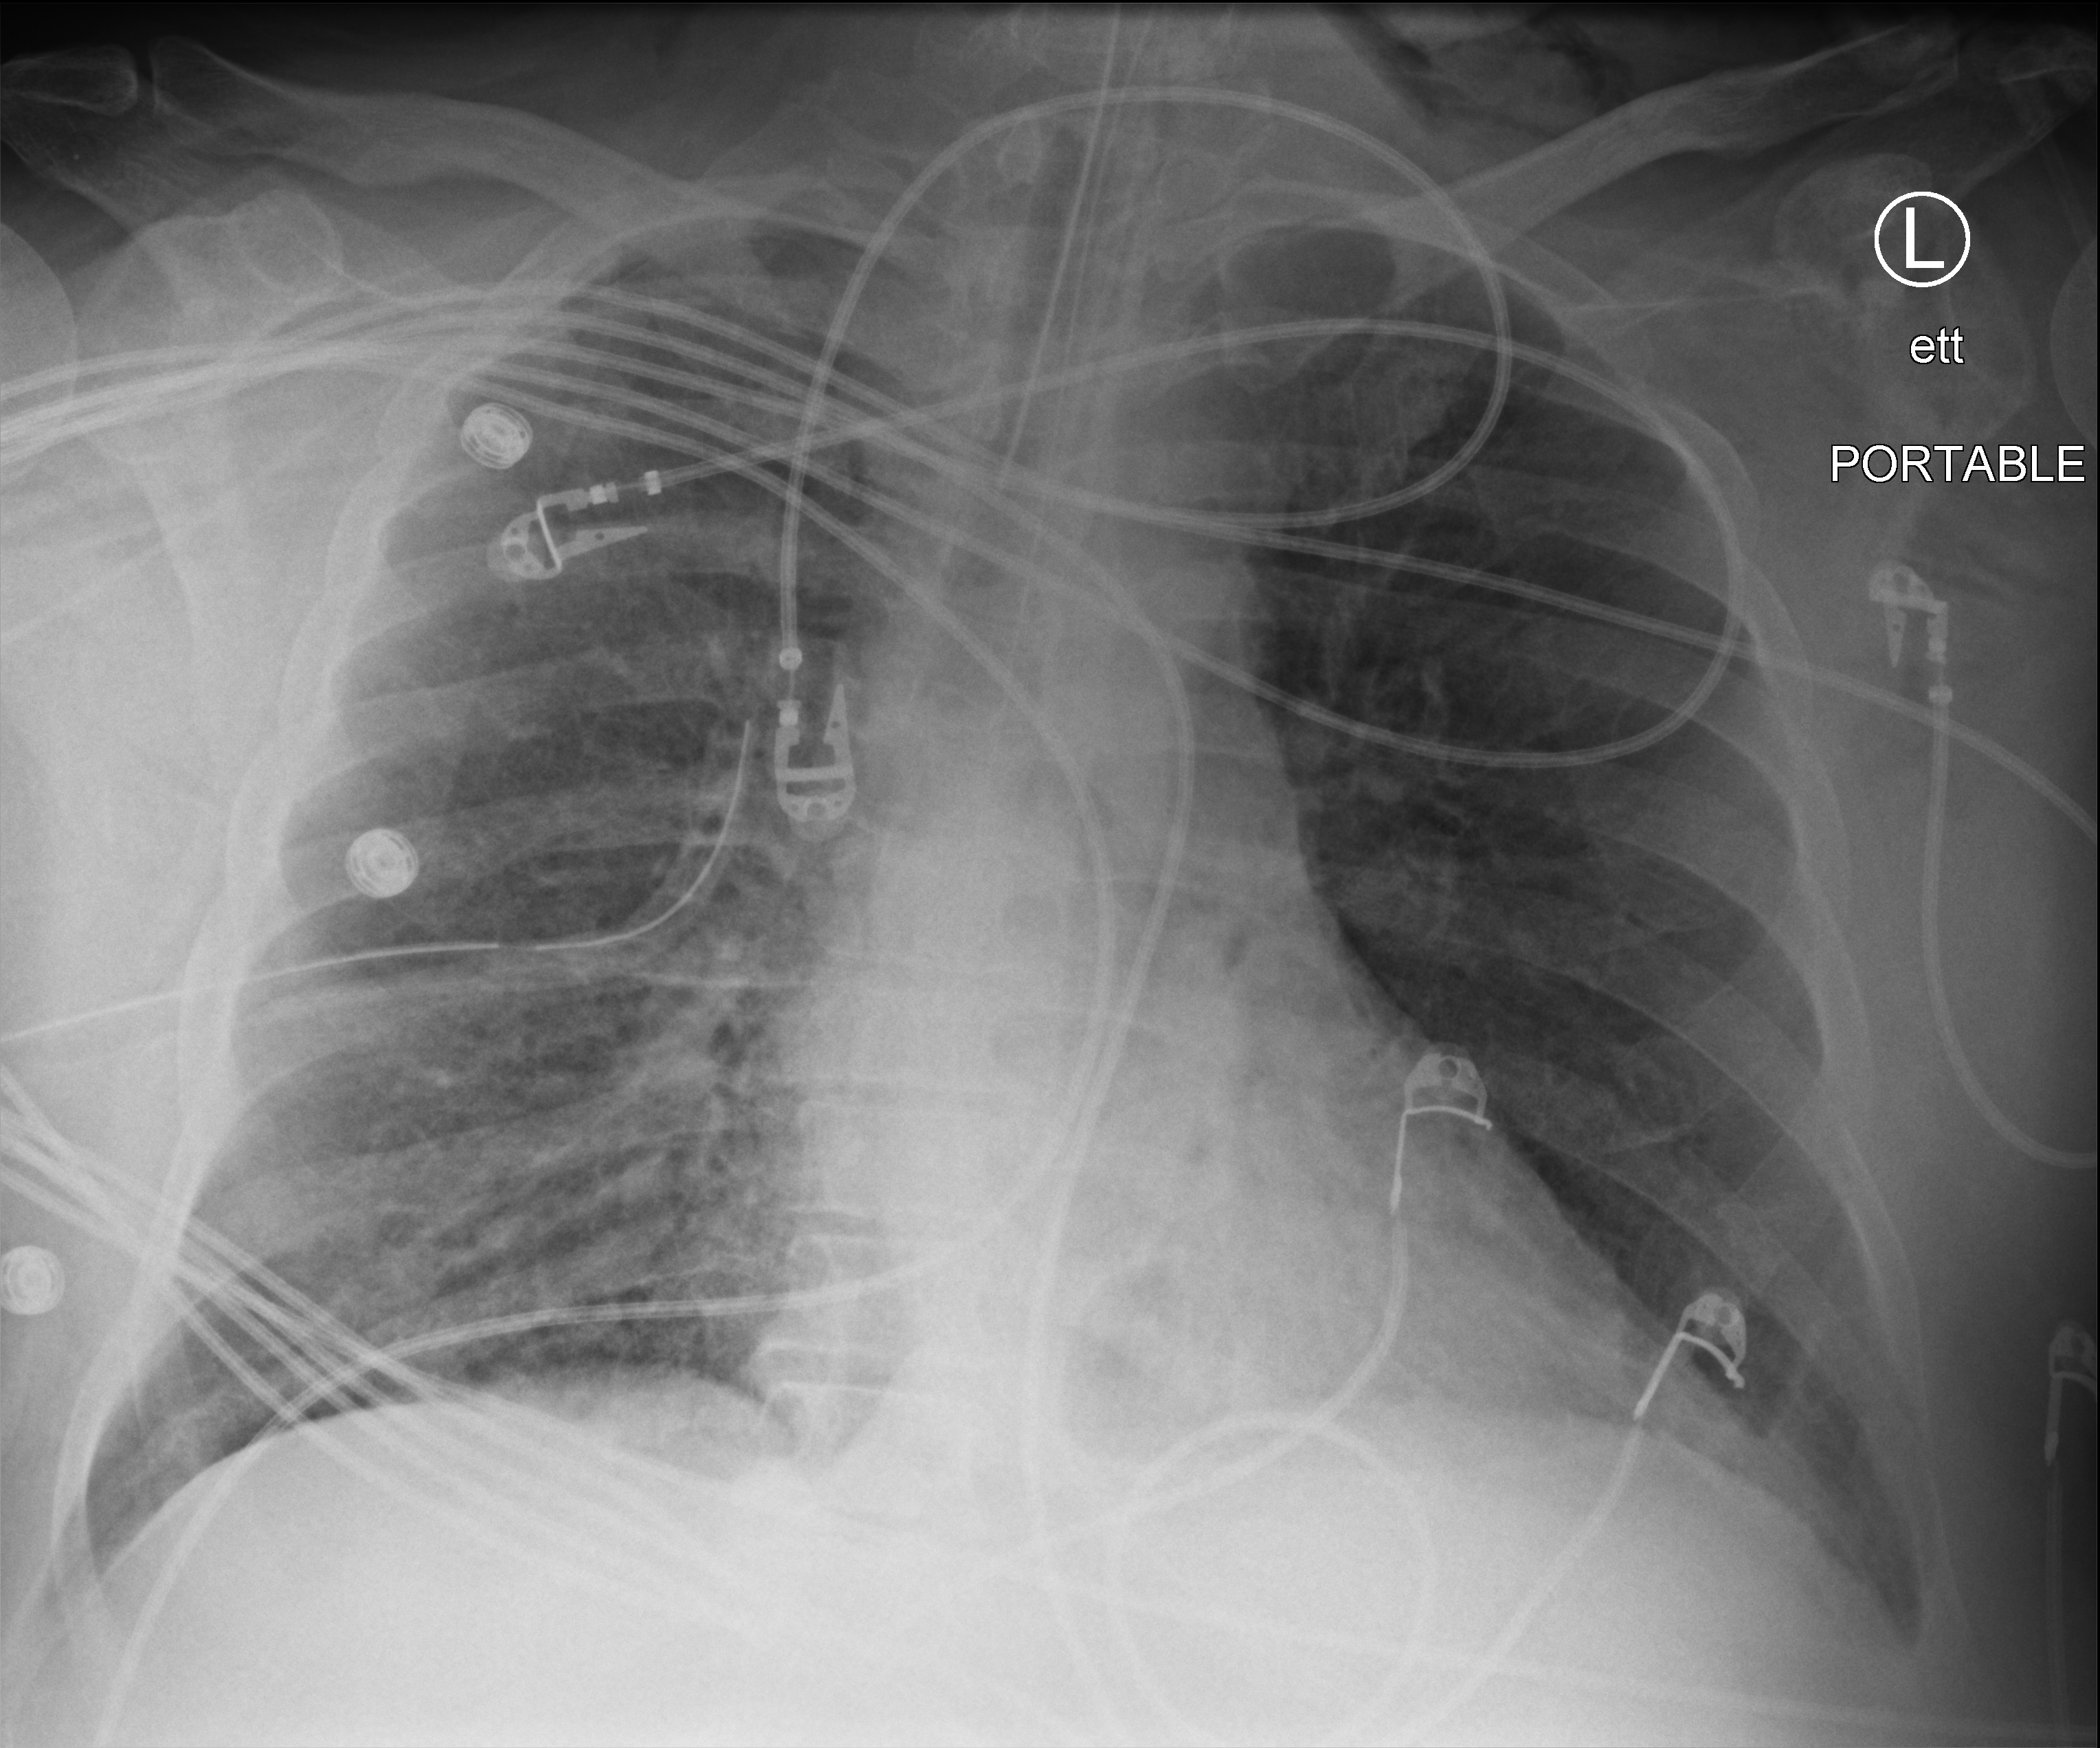
Portable chest radiograph; anteroposterior (AP) projection. Adult patient hospitalised with COVID-19, age 18–59 years.
Admission-level facts for this patient (not findings on this image; timing relative to this image not recorded): mechanically ventilated during this hospital stay: yes.